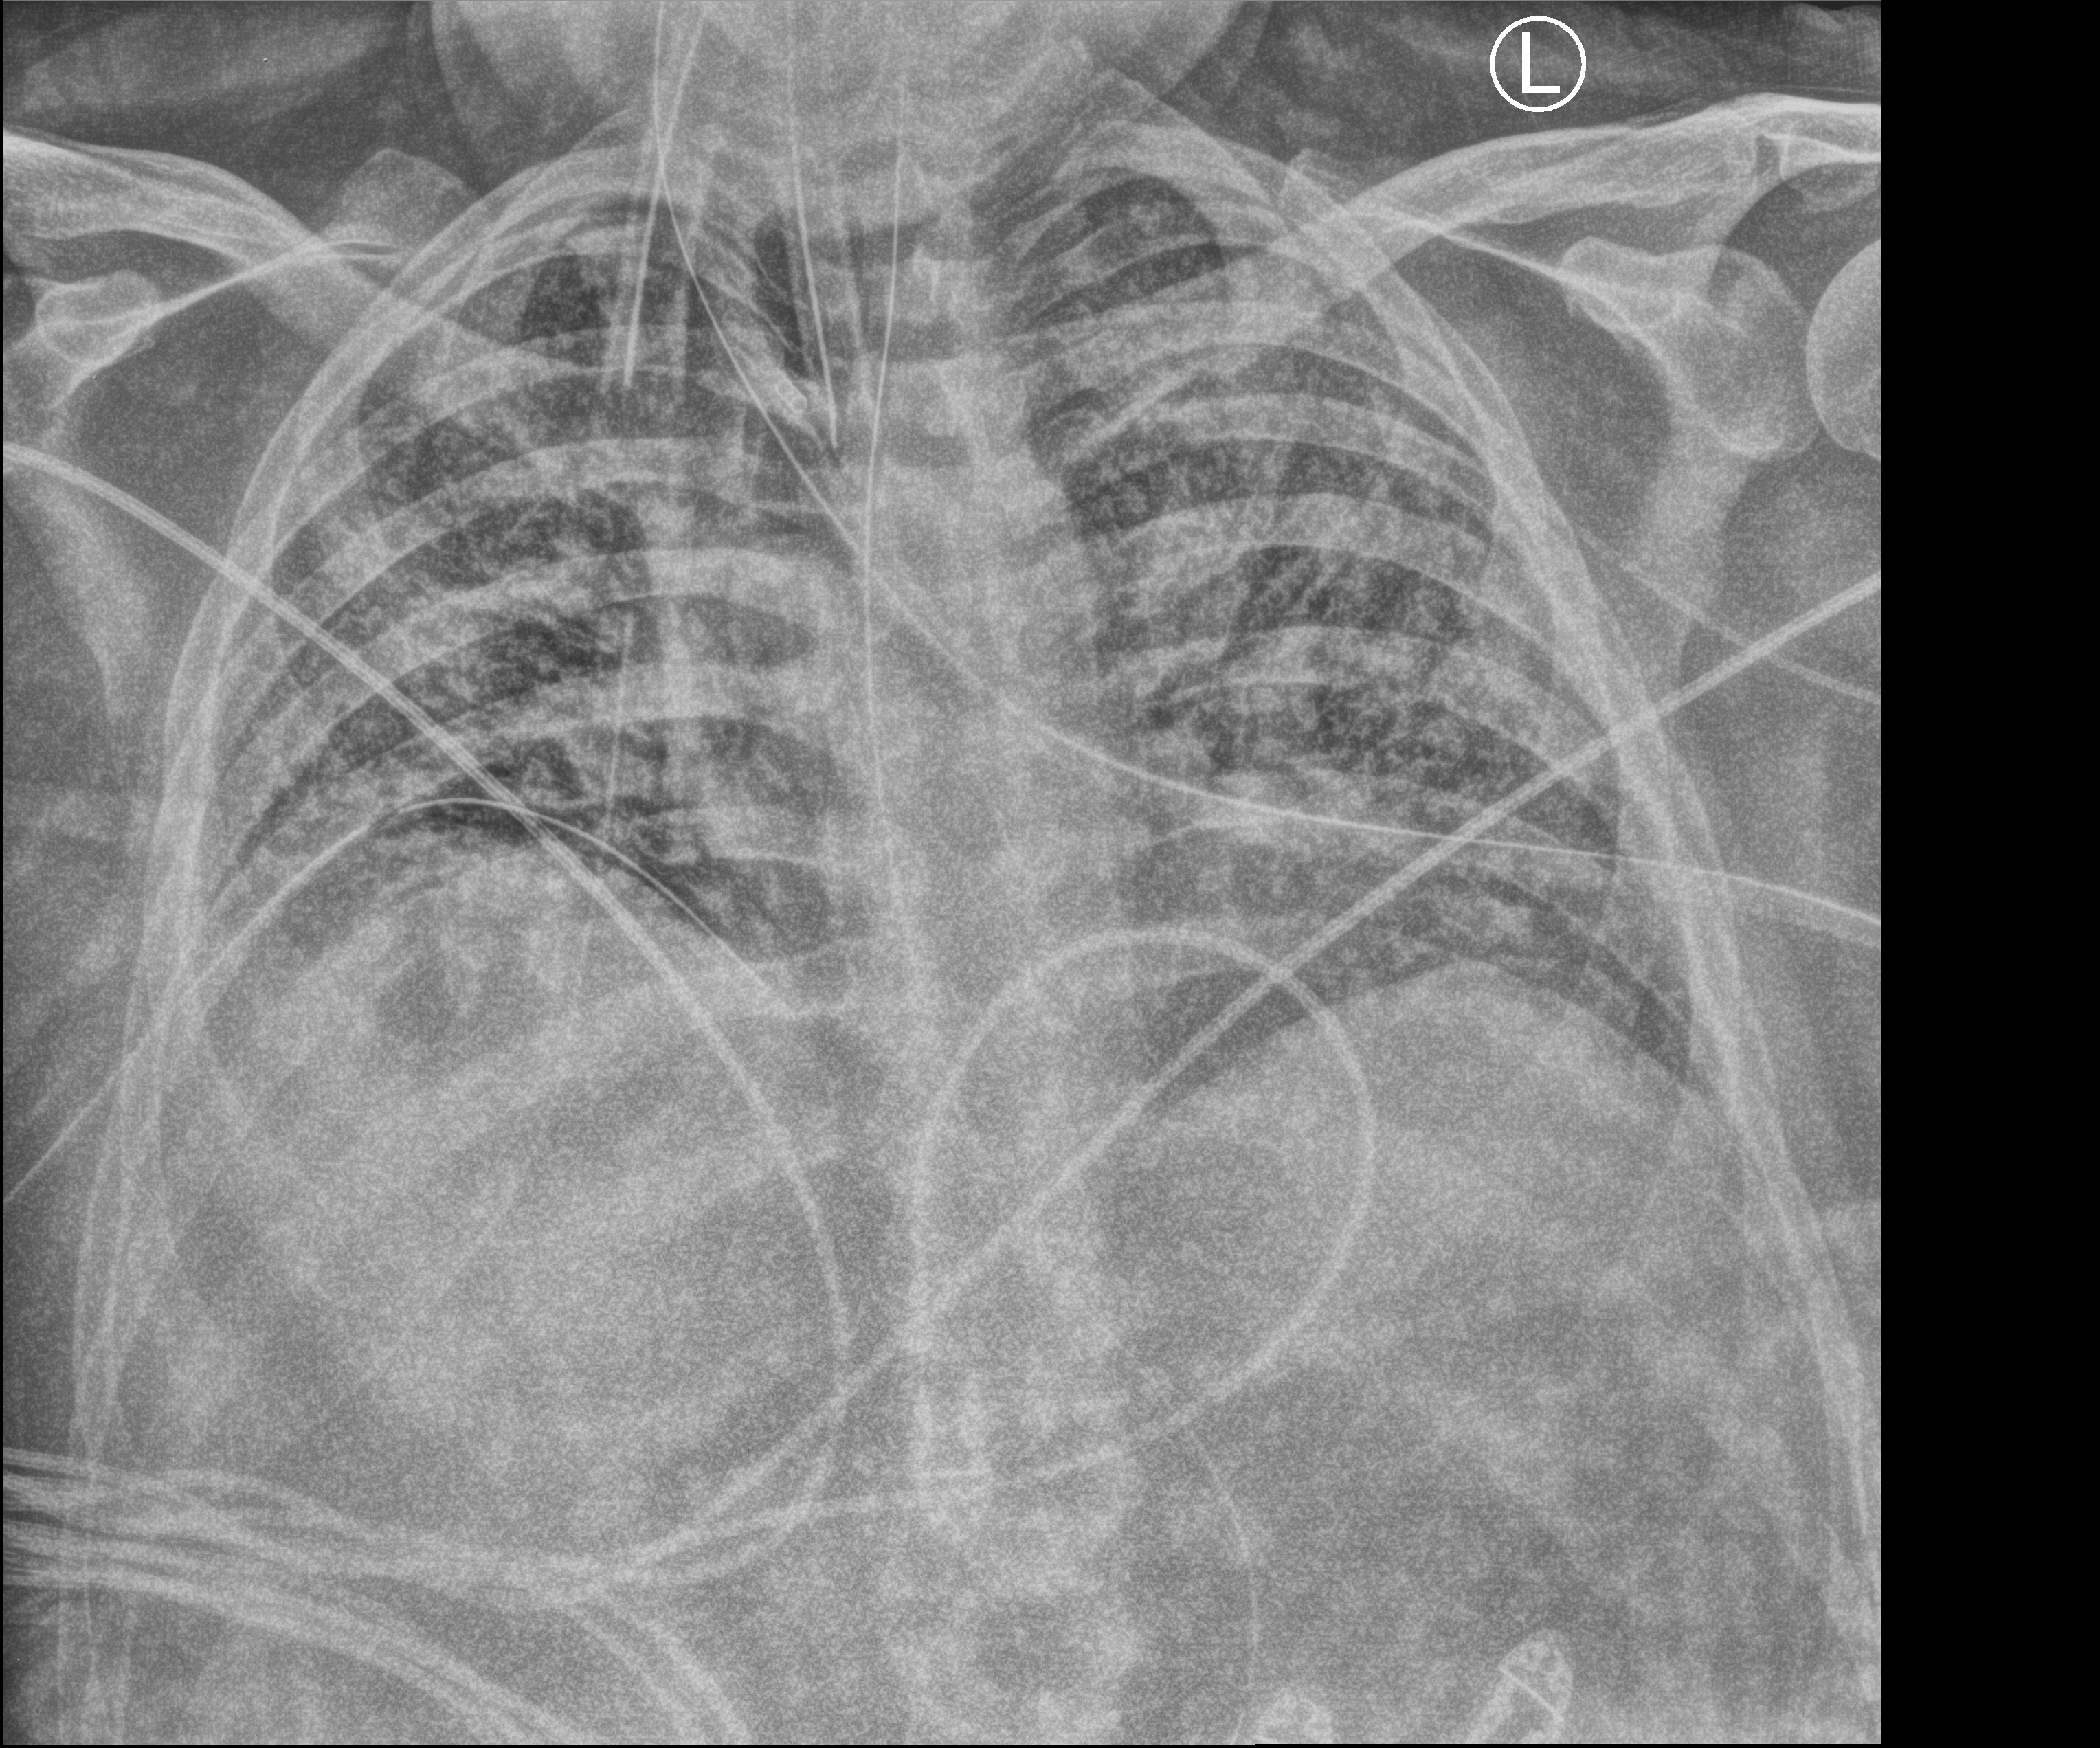
Bedside chest radiograph (computed radiography). Patient hospitalised with COVID-19; male, aged 18–59 years.
Hospital-stay facts (about this admission, not read from this image; timing relative to this image not recorded):
- length of hospital stay: 80 days
- hypertension (admission record): yes
- mechanically ventilated during this hospital stay: yes